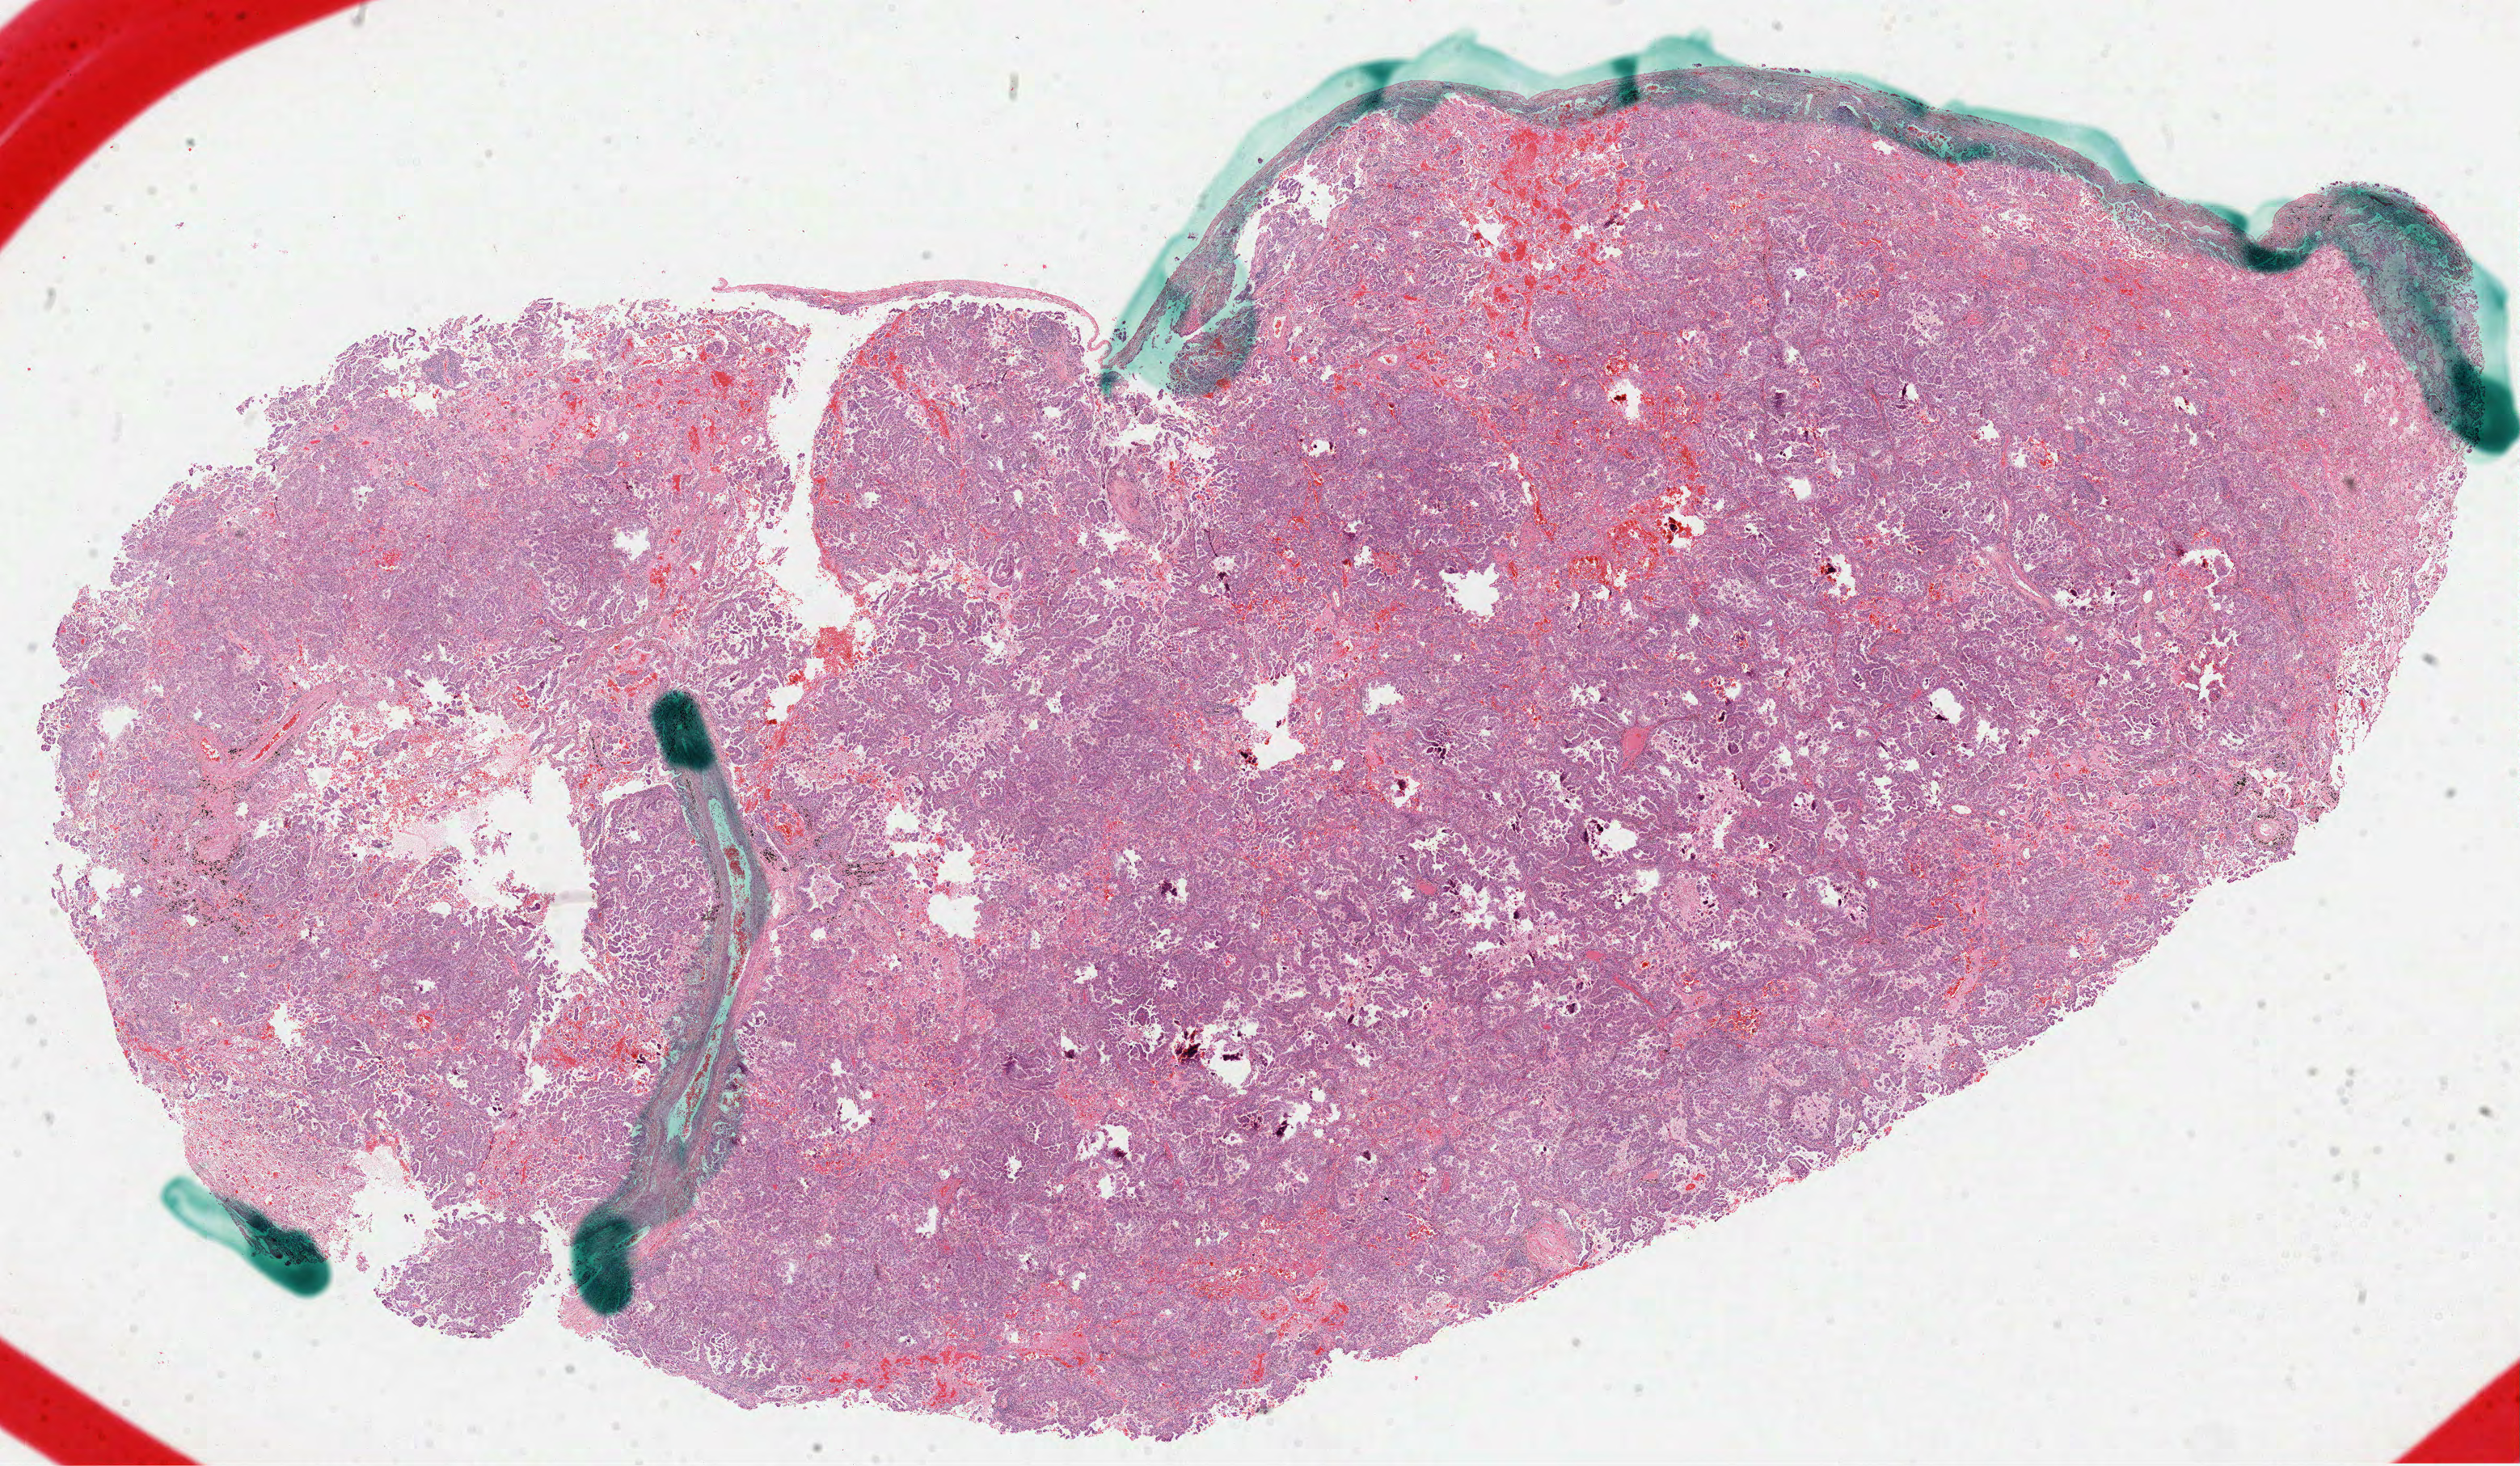
Whole-slide histology image, Hematoxylin and eosin (H&E) stained — shown as a low-resolution overview of the whole scanned area (about 25.1 x 14.6 mm), formalin-fixed paraffin-embedded (FFPE) diagnostic section, sample: primary tumour, lung. Male patient; age at initial diagnosis 70 years.
- laterality: right
- diagnosis: Adenocarcinoma, NOS (middle lobe, lung)
- AJCC pathologic stage: IIA (7th edition)